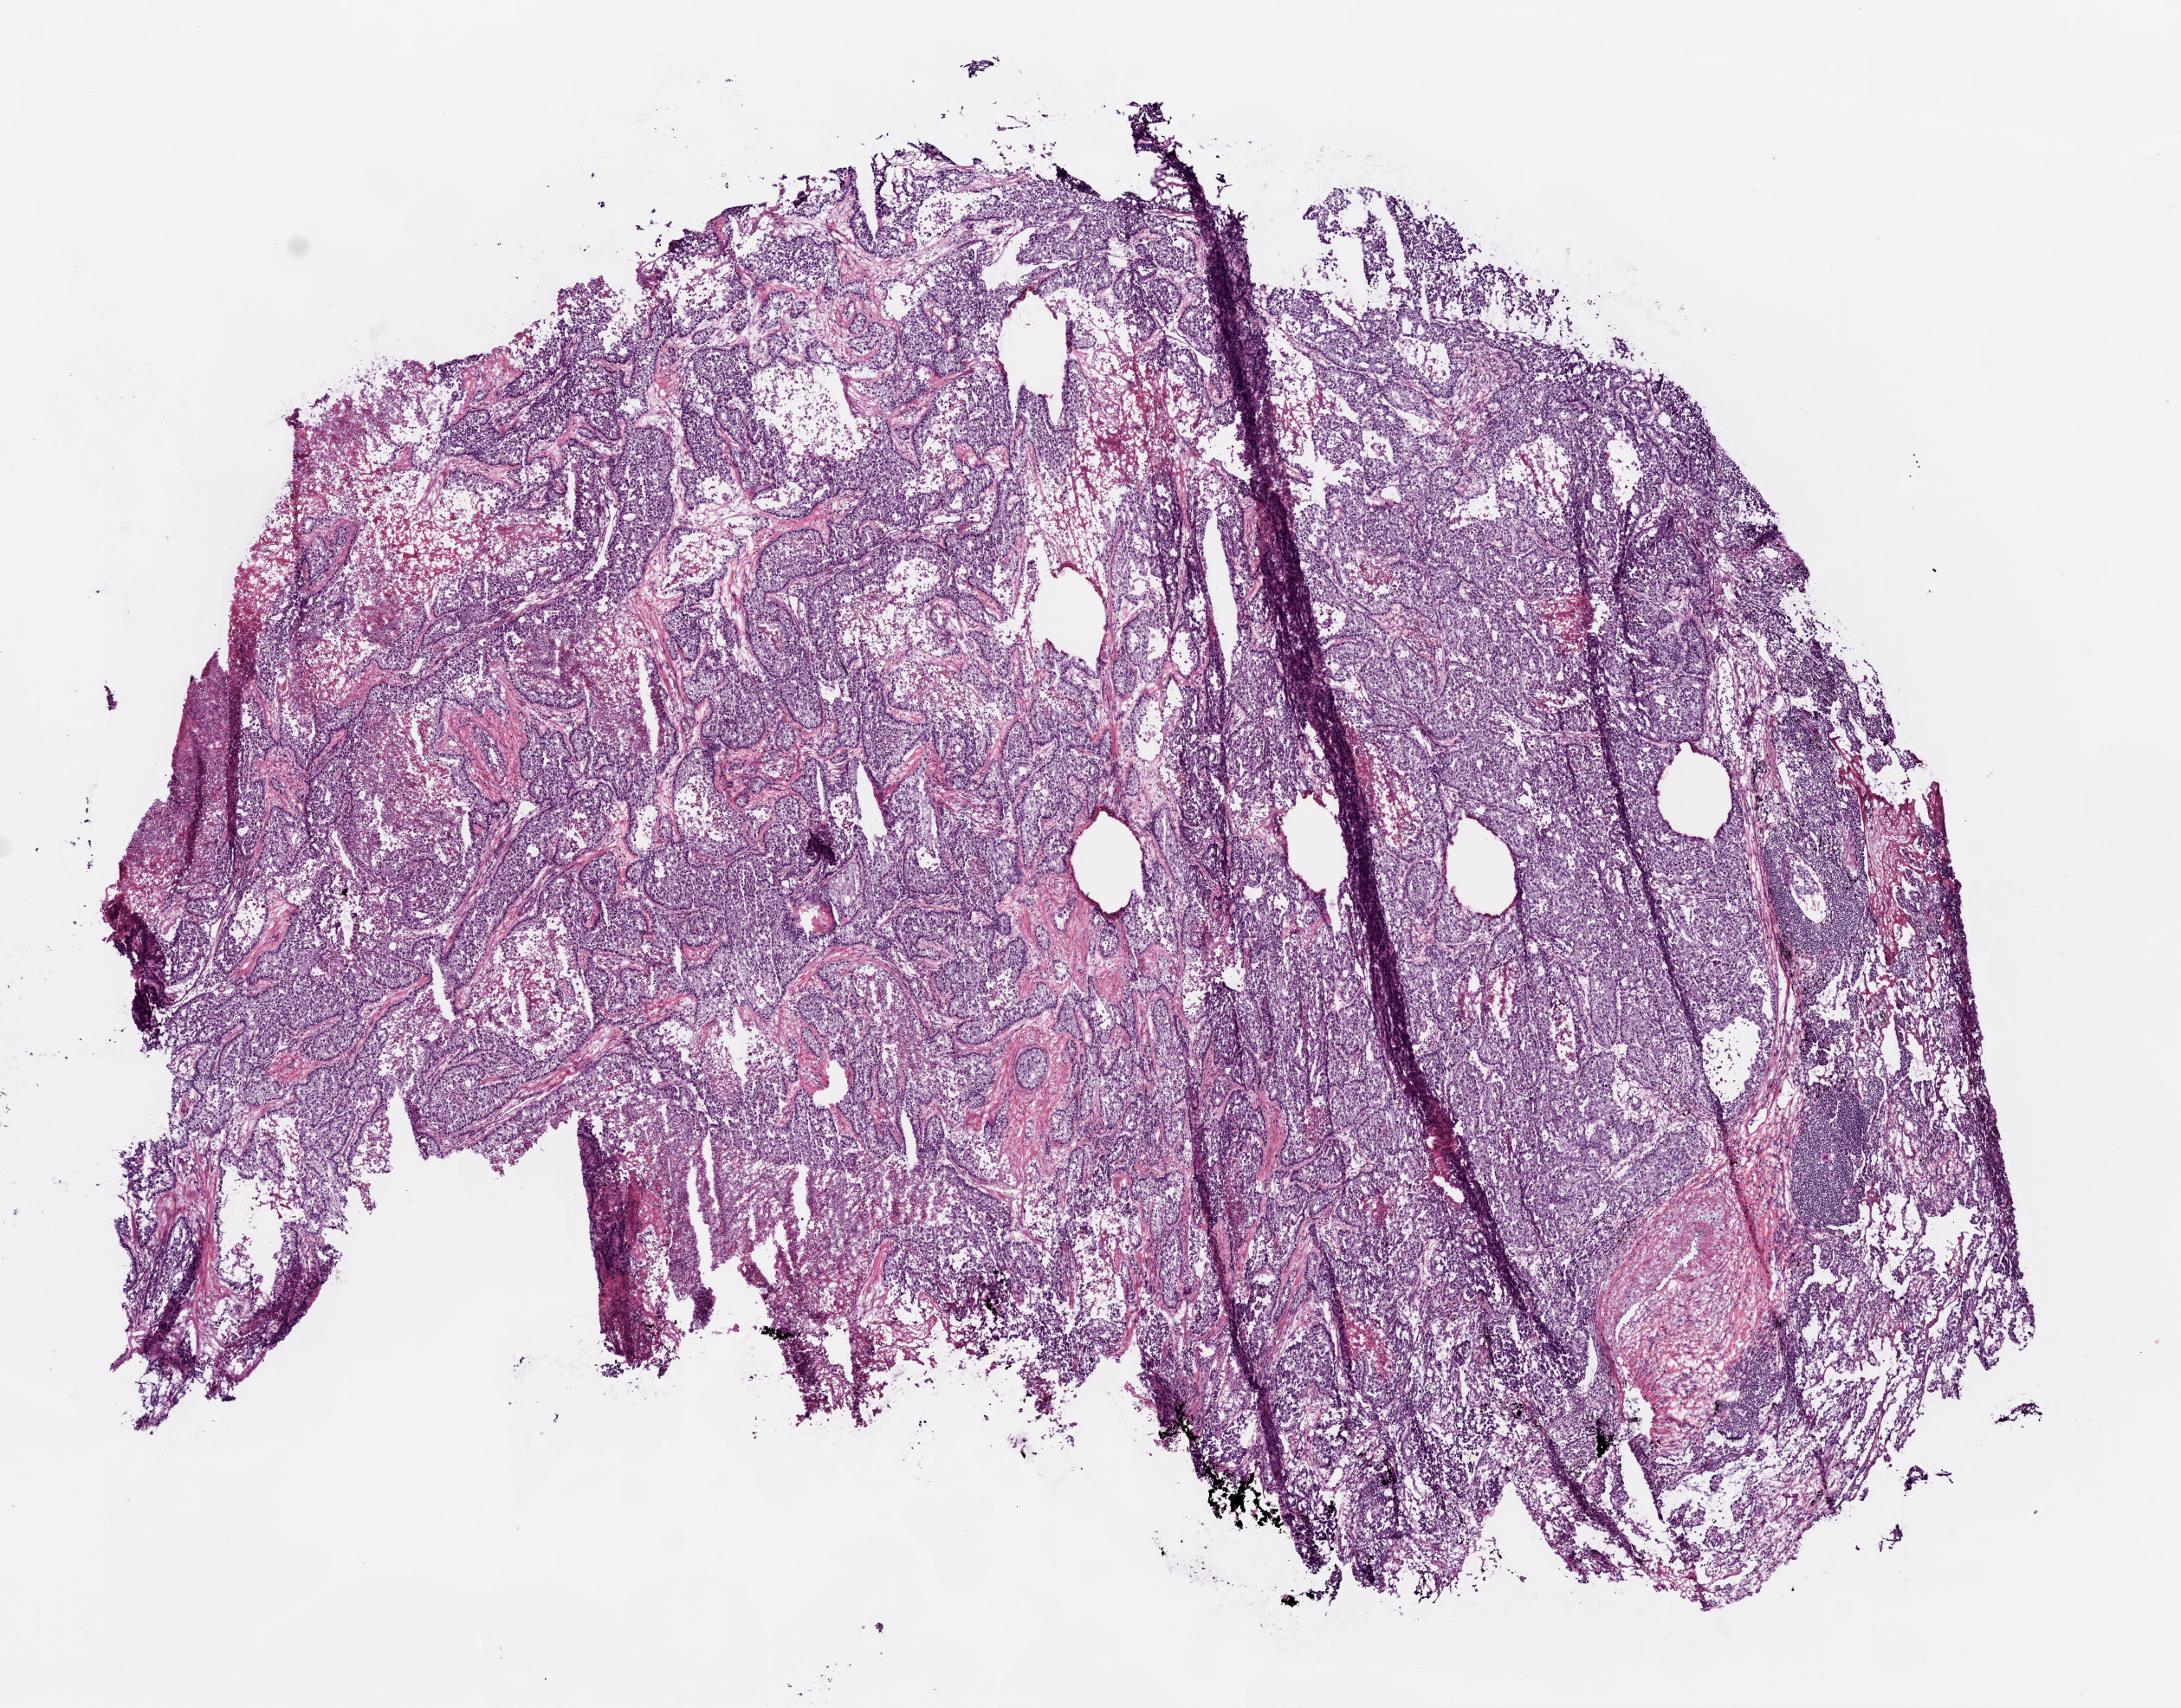
Whole-slide histology image, Hematoxylin and eosin (H&E) stained, whole scanned area (about 10.2 x 8.0 mm) shown as a low-resolution overview; frozen section; lung, primary tumour sample. Female, age 50 years at initial diagnosis. Composition of this section per pathologist review: tumour cells 75%, tumour nuclei 75%, normal cells 5%, stromal cells 10%, necrosis 10%.
AJCC pathologic stage: IIA (7th edition). Laterality: left. Diagnosis: Adenocarcinoma, NOS (lower lobe, lung).